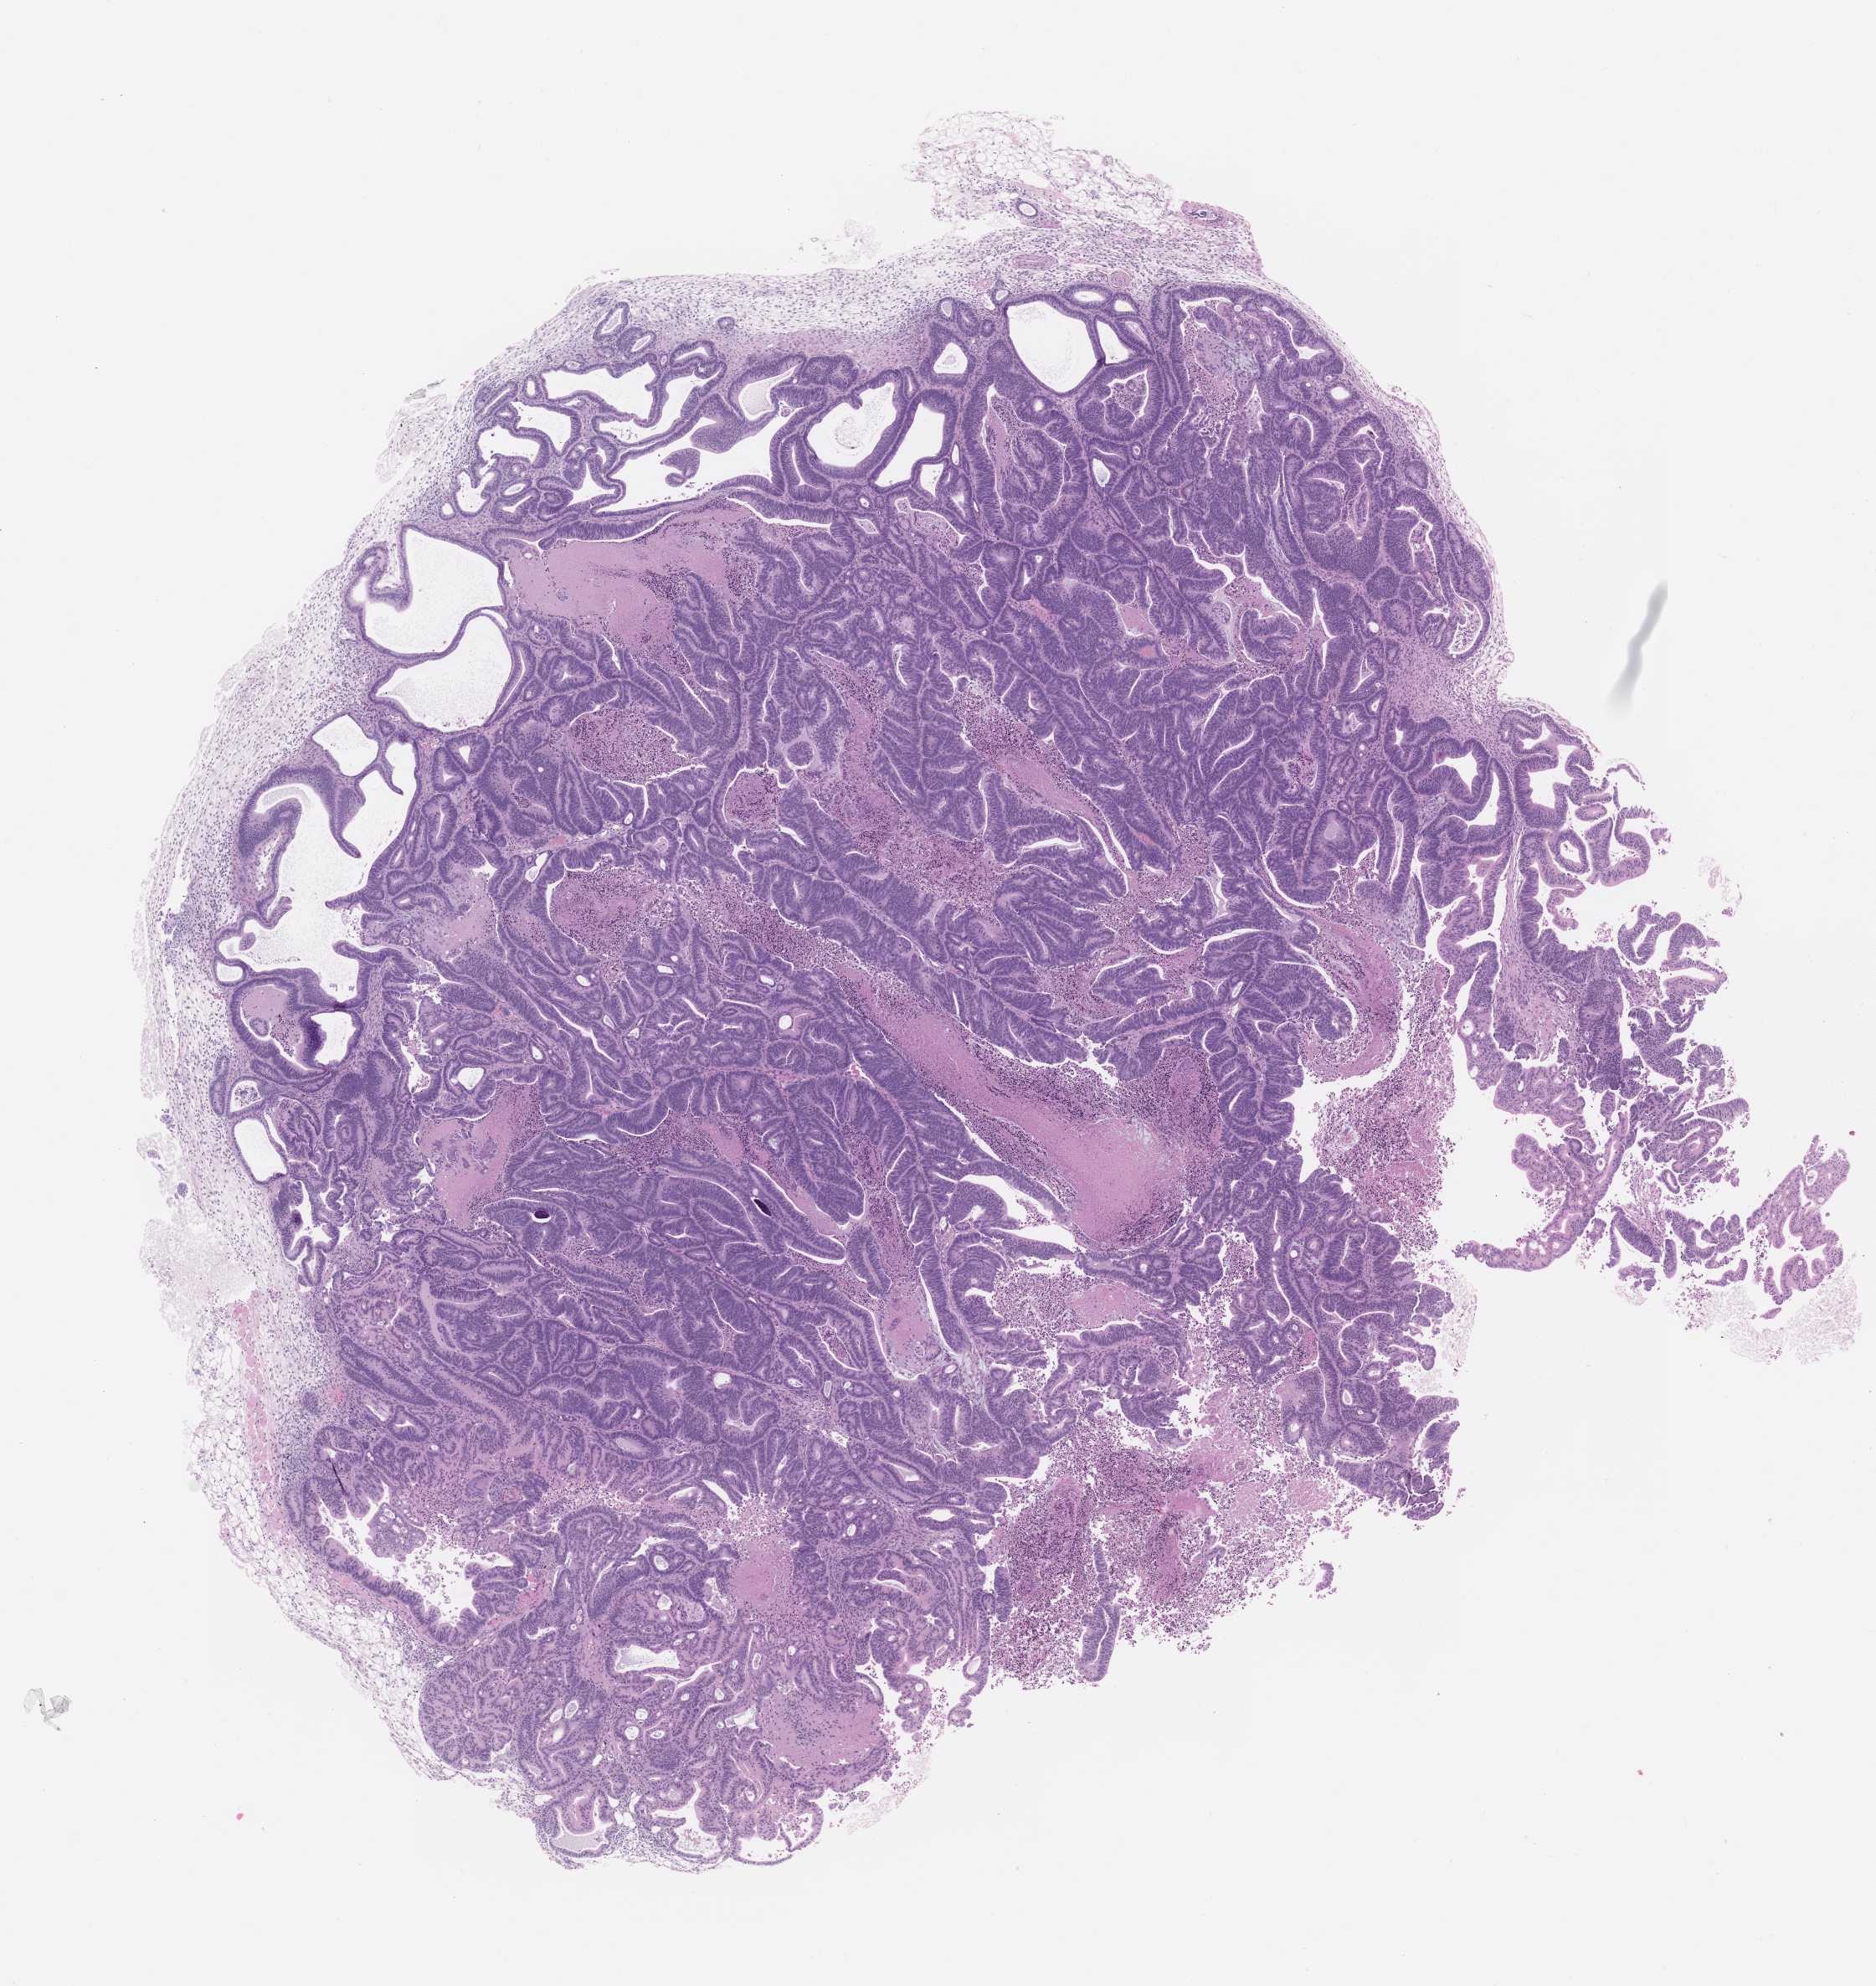
H&E whole-slide image of a patient-derived xenograft (PDX) tumor grown in a mouse, passage 1, whole scanned area (about 9.0 x 9.5 mm) shown as a low-resolution overview, formalin-fixed, paraffin-embedded (FFPE) tissue, tumor site category: colon.
- originating patient diagnosis: Colon Adenocarcinoma